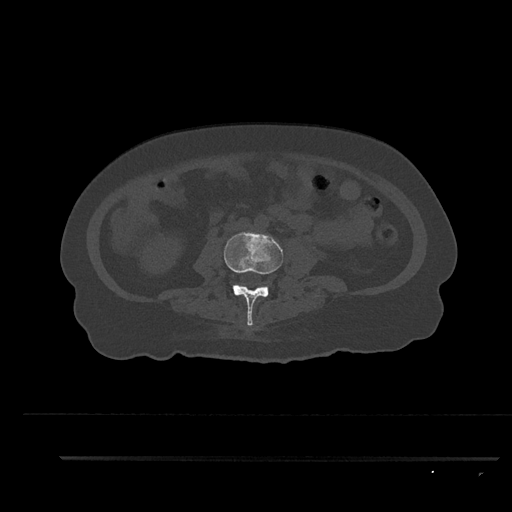
CT including the spine, one axial slice. Slice 73 of 797 in the series (ordered by position). Reconstruction kernel Br40s/3. 120 kVp. Bone window (W 1800 / L 400 HU). 0.5 mm slice thickness. 512 × 512 image matrix. Female patient, age 44 years. Case-level facts recorded for this patient, not image findings: primary cancer: renal; vertebrae with lytic lesions (as recorded): L1.
Structures marked on this image (semi-automatic segmentation, software-assisted and operator-edited):
- L3 vertebra: bounding box (x1, y1, x2, y2) in pixels: (224, 232, 284, 326)